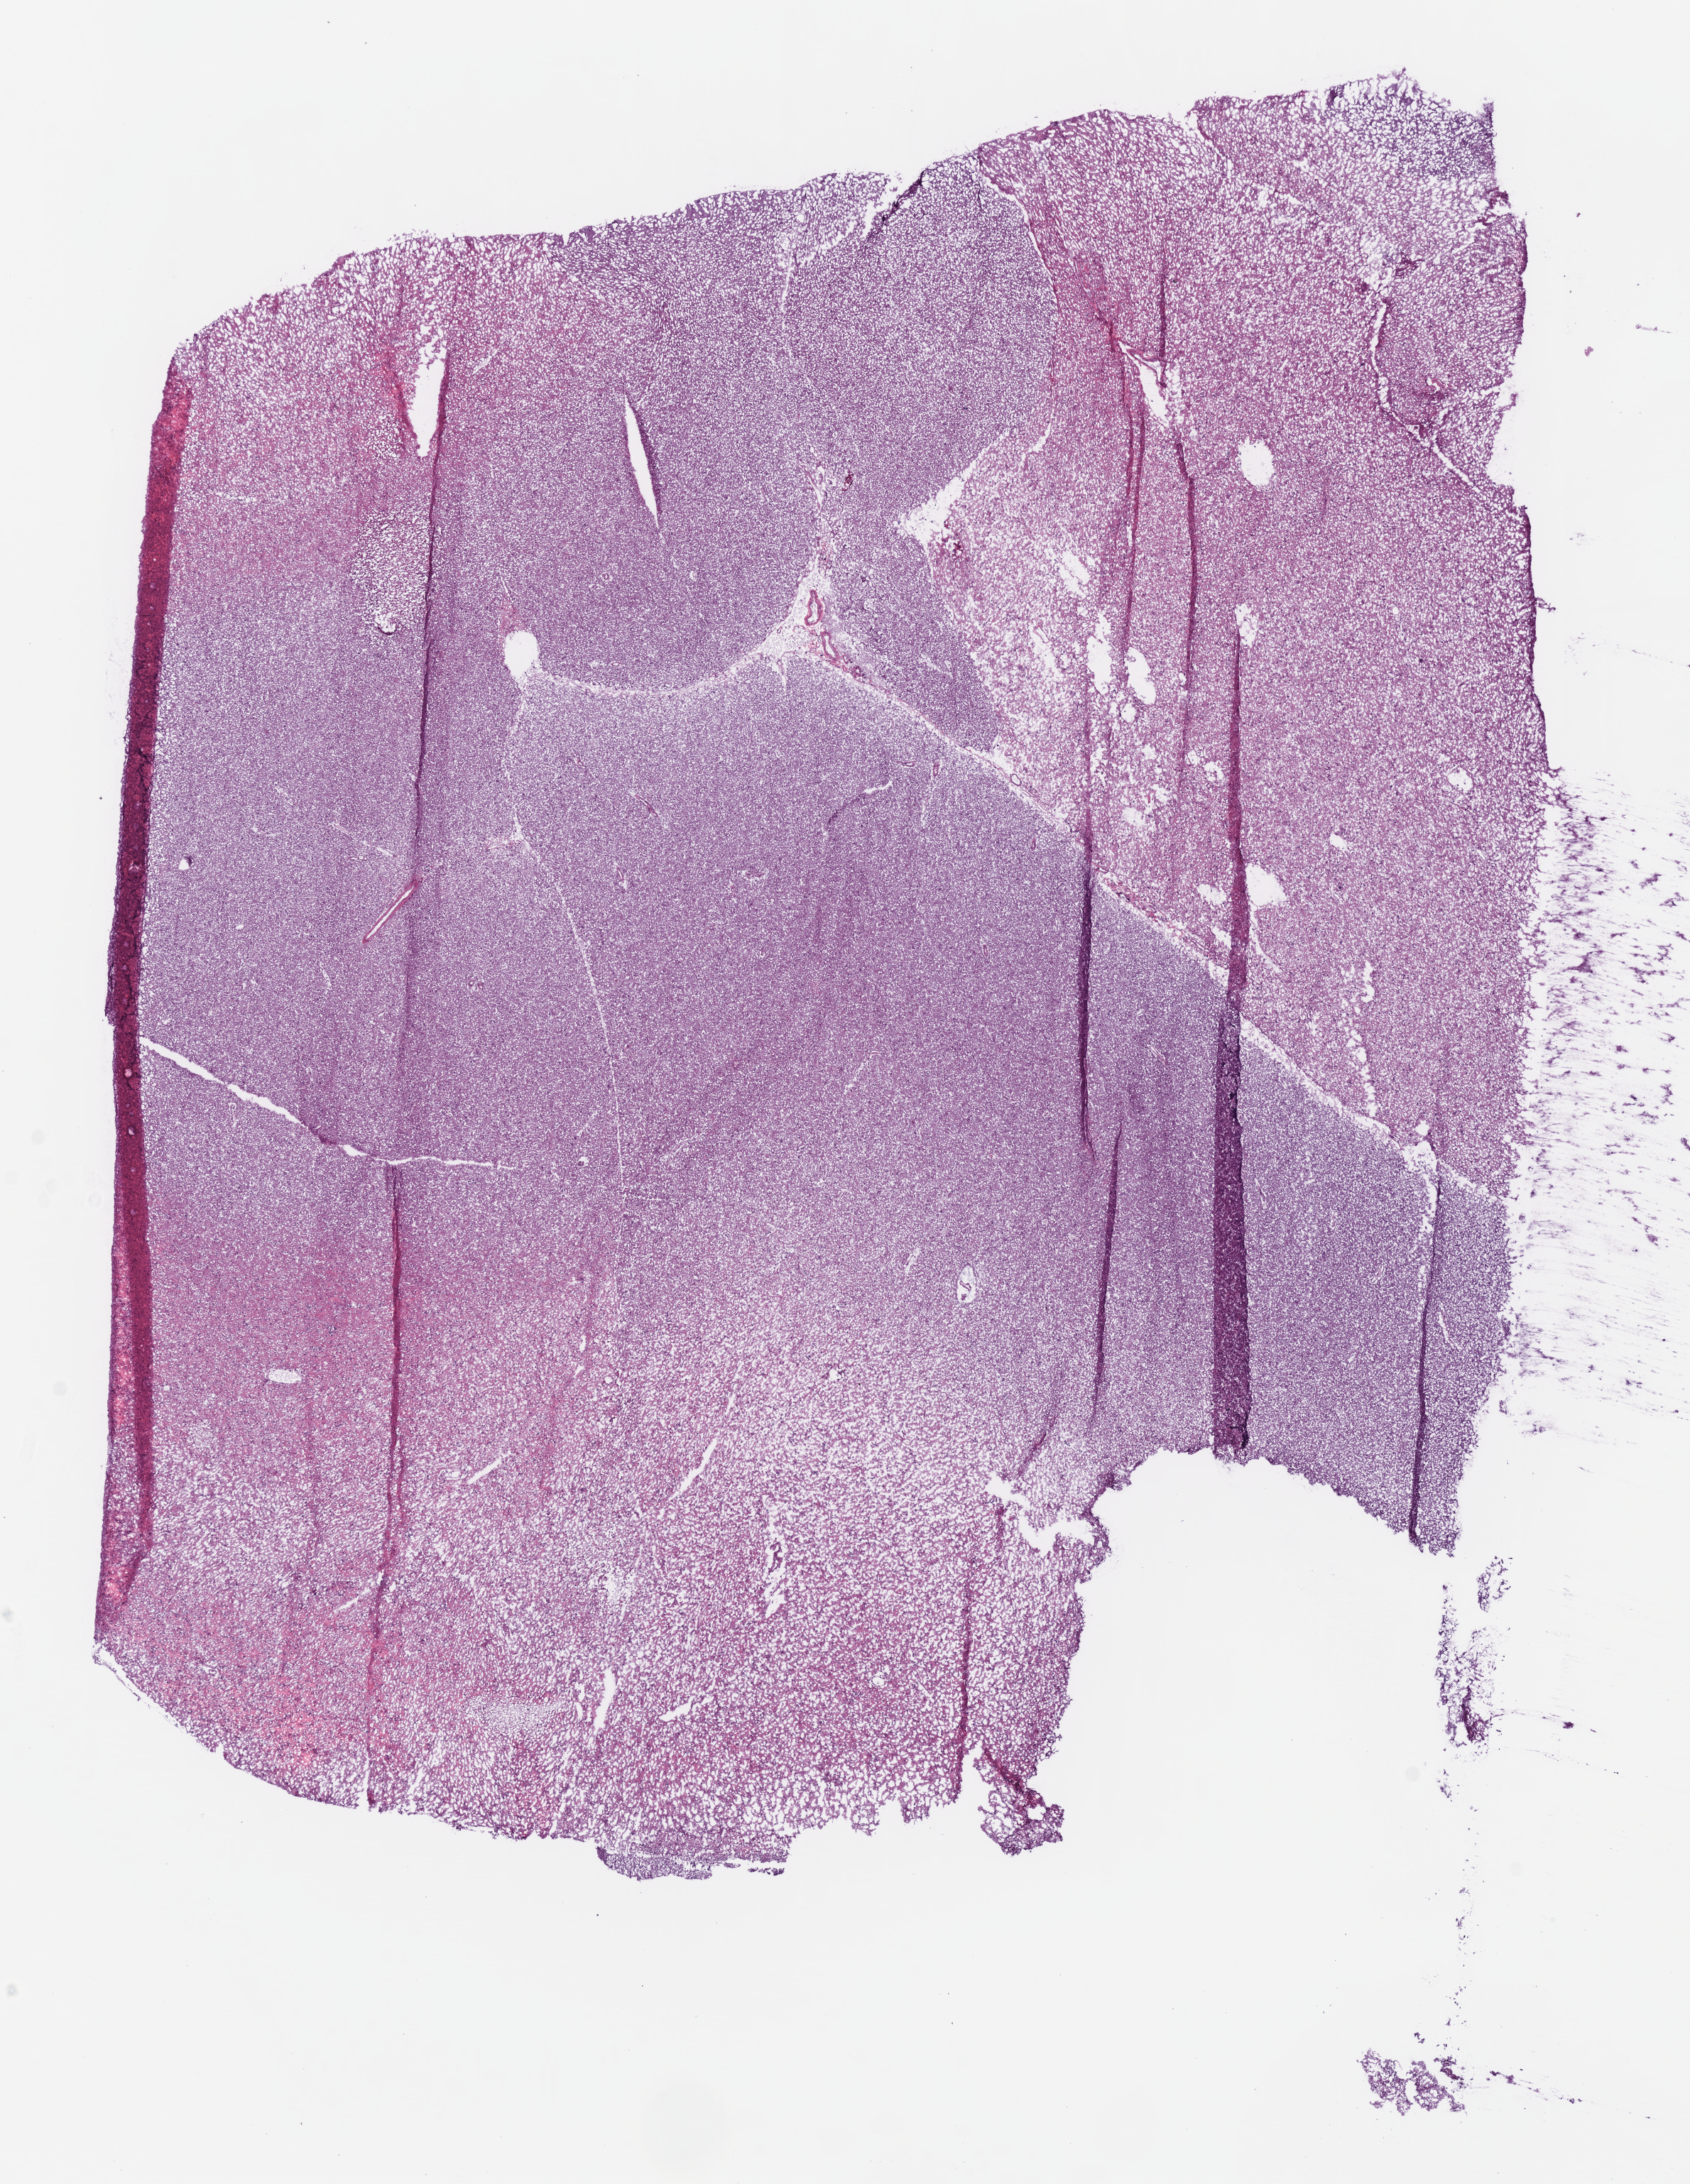
Whole-slide histology image, H&E-stained, shown as a low-resolution overview of the whole scanned area (about 9.4 x 12.1 mm). Frozen section from the bottom of the tissue portion. Brain, primary tumour sample. Male patient; age at initial diagnosis 60 years. Histologic grade: G3 (poorly differentiated). Pathologist review of this section (percent, as recorded): tumour cells 100%, tumour nuclei 60%, normal cells 0%, stromal cells 0%, necrosis 0%.
Diagnosis: Oligodendroglioma, anaplastic (cerebrum).